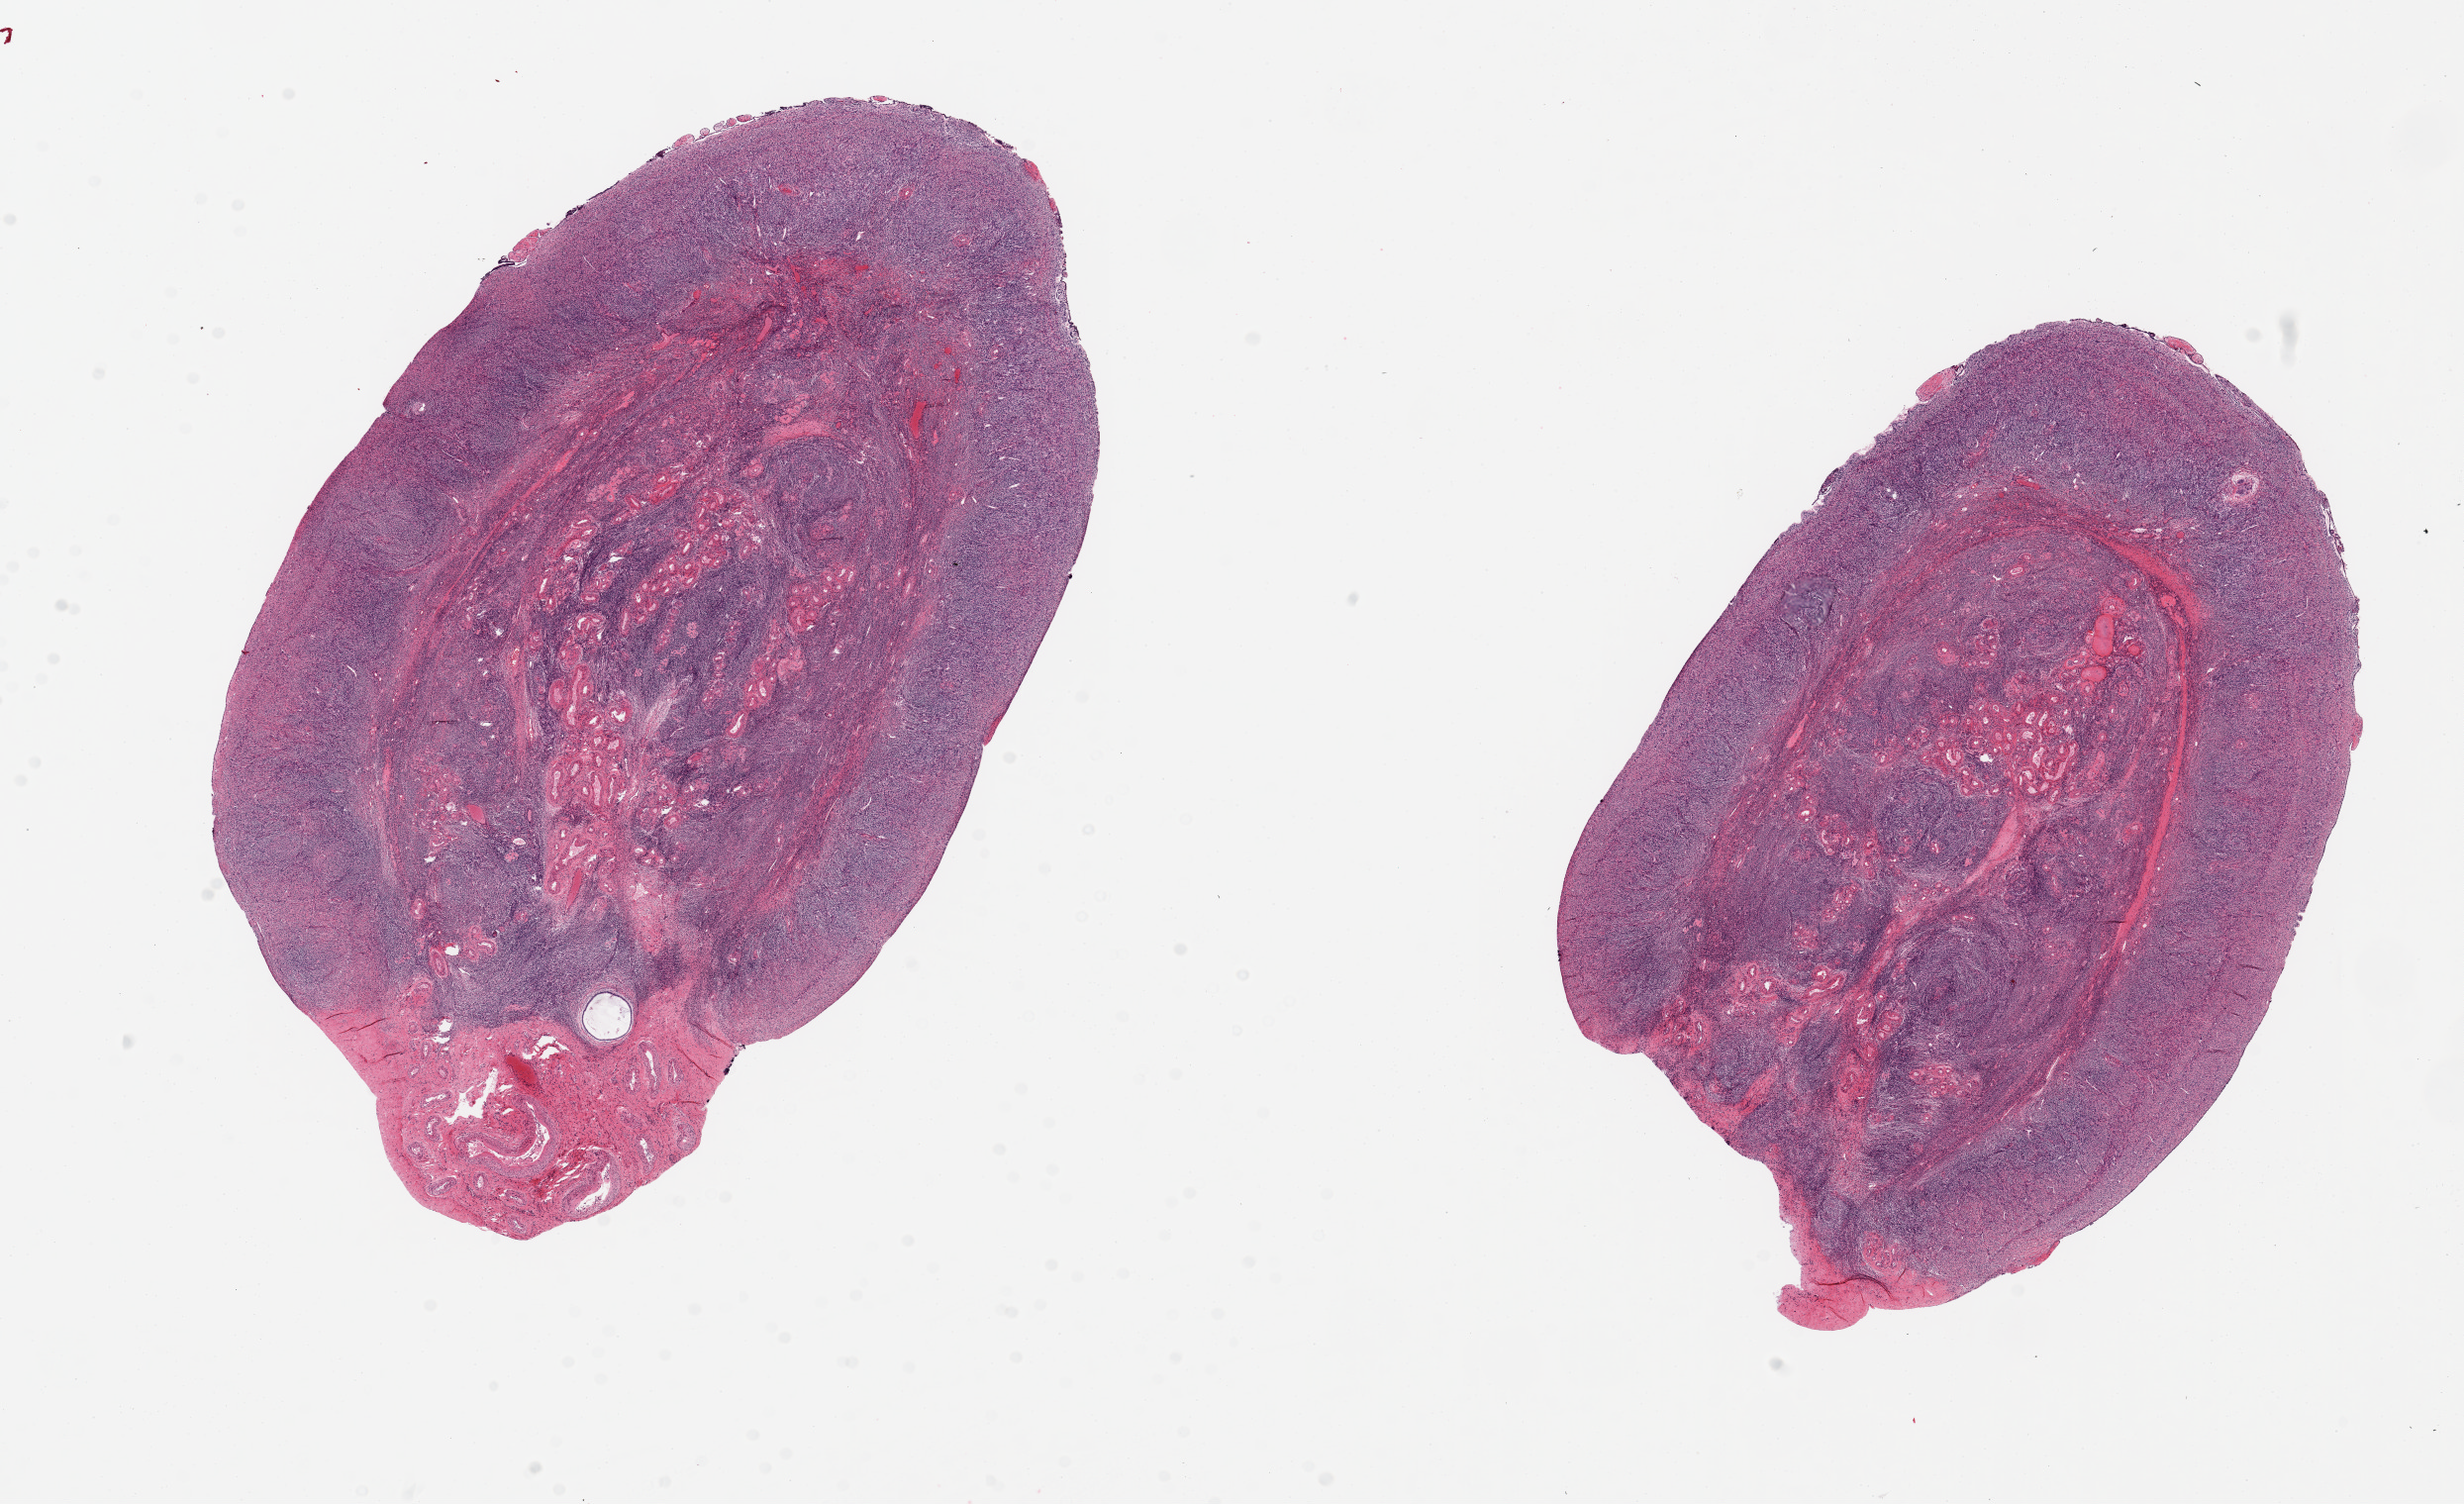
Whole-slide image, H&E stain, brightfield — whole scanned area (about 19.7 x 12.0 mm, from a 20x scan) shown as a low-resolution overview; PAXgene-fixed, paraffin-embedded tissue; sampled site (target tissue): ovary; donor tissue sample. Donor sex: female.
Reviewer comment on this tissue sample: 2 pieces ~9x5mm. Post menopausal involution.